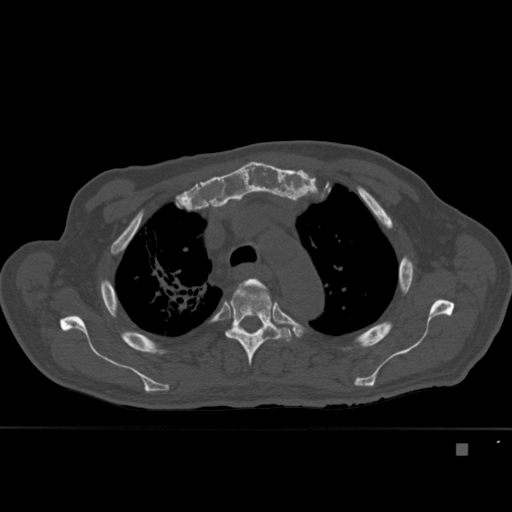
CT including the spine, one axial slice; slice 322 of 451 in the series (ordered by position); bone window (W 1800 / L 400 HU); 1.5 mm slice thickness; 512 × 512 image matrix. Patient: male, 75 years. From the clinical record (not read from this slice): primary cancer: prostate.
Annotated regions visible in this slice (semi-automatically segmented with operator editing):
- T3 vertebra: bounding box <234,278,270,297> (left, top, right, bottom; pixels)
- T4 vertebra: <225,278,292,366>
- T5 vertebra: <261,323,263,328>